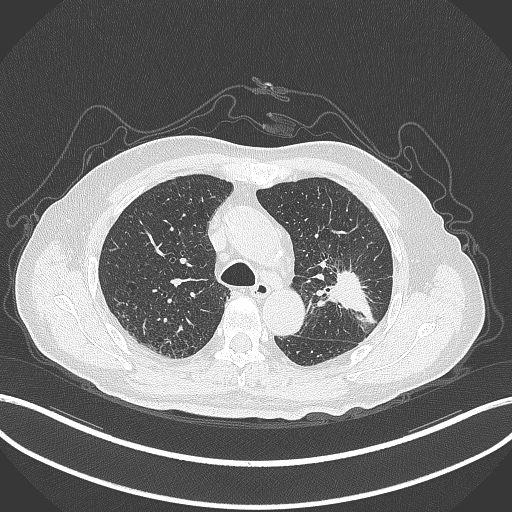
Chest CT, one axial slice. Slice 201 of 331 in the series (ordered by position). 120 kVp. Lung window (W 1500 / L -600 HU). 1 mm slice thickness. 512 × 512 image matrix, field of view 400 × 400 mm. Patient: male, 79 years. From the clinical record (not read from this slice): clinical TNM (as recorded): T2a N1 M1; histopathological grade: G3.
Annotated regions visible in this slice (bounding box drawn by a radiologist):
- lung tumour (recorded histology: adenocarcinoma): box from (x=323, y=265) to (x=376, y=329) px